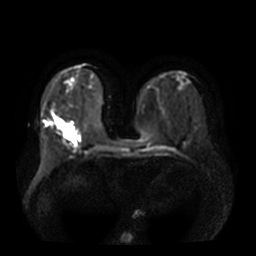
Breast MRI, one axial slice. Slice 13 of 36 in the series (ordered by position). Diffusion-weighted series; image 2 of 4 stored at this slice position (different b-values; order by instance number). 3 T. 256 × 256 image matrix. Female patient.
Structures marked on this image (outlined manually by an expert reader):
- tumour on diffusion-weighted imaging: box from (x=56, y=121) to (x=72, y=137) px